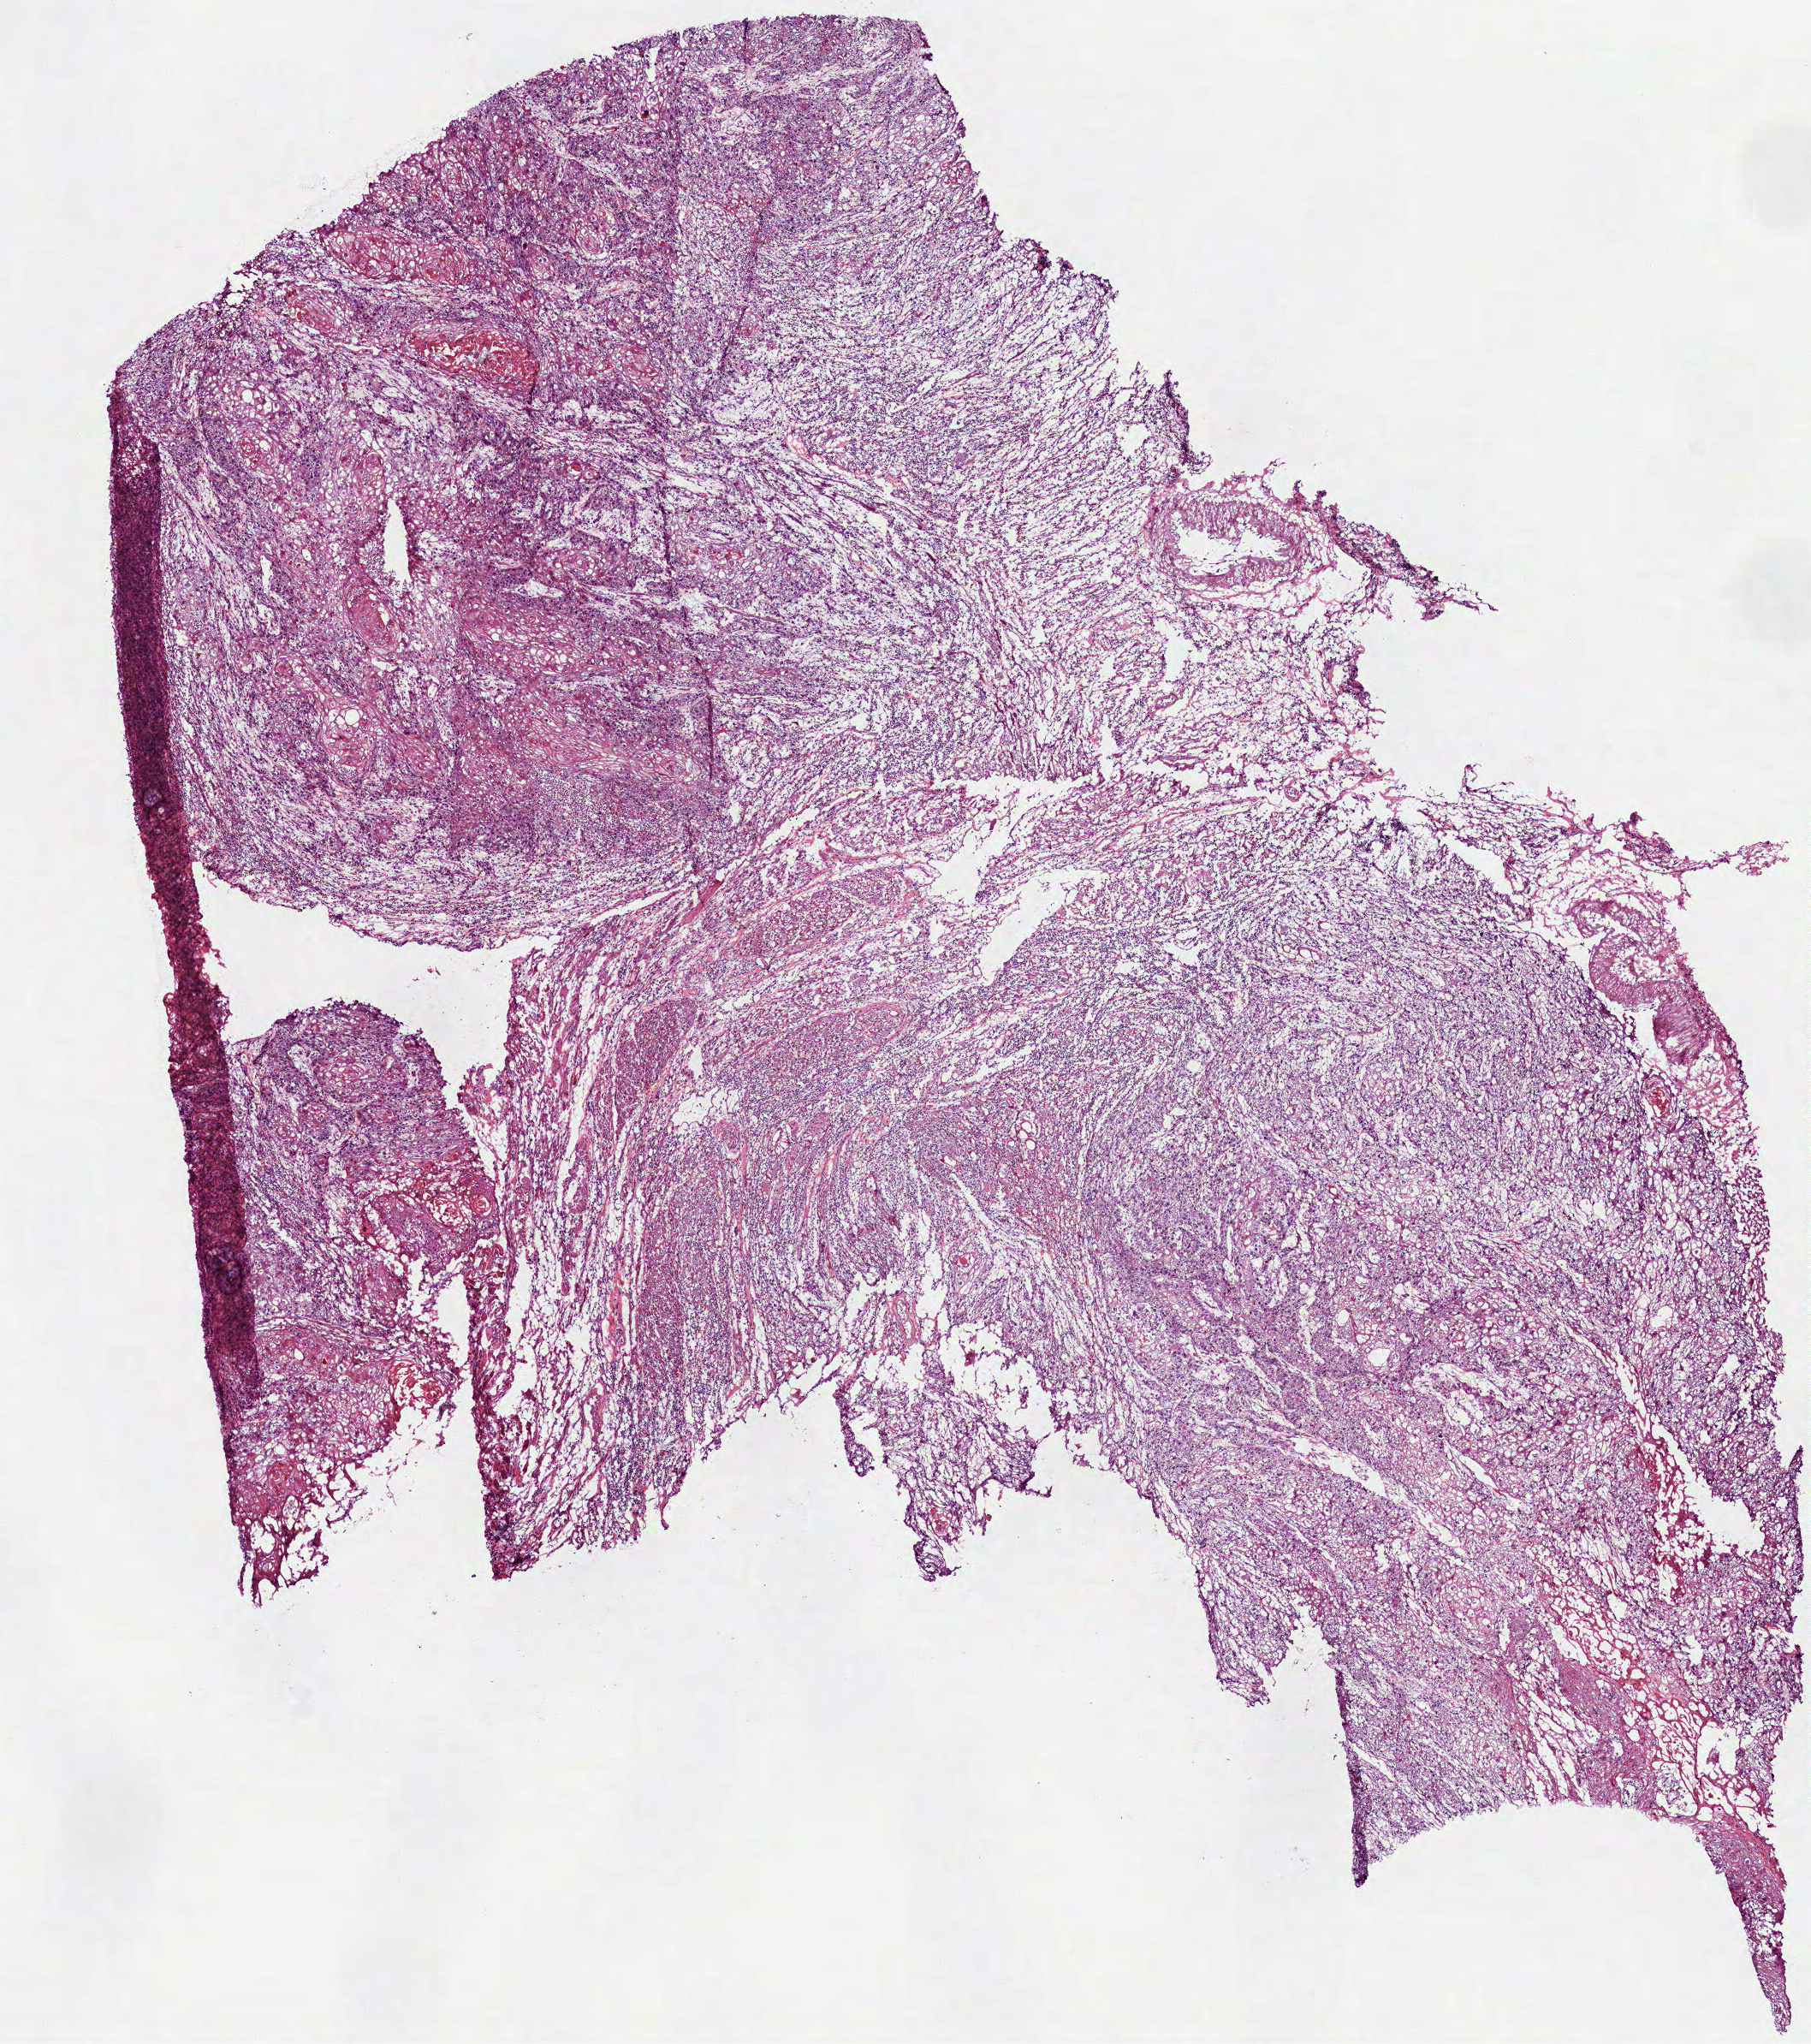
H&E whole-slide image — low-resolution overview of the scanned area, about 8.5 x 9.6 mm (slide scanned at 40x), frozen section, sample: primary tumour, head and neck. Male patient; age at initial diagnosis 53 years.
Histologic diagnosis: Squamous cell carcinoma, NOS (tongue, NOS).